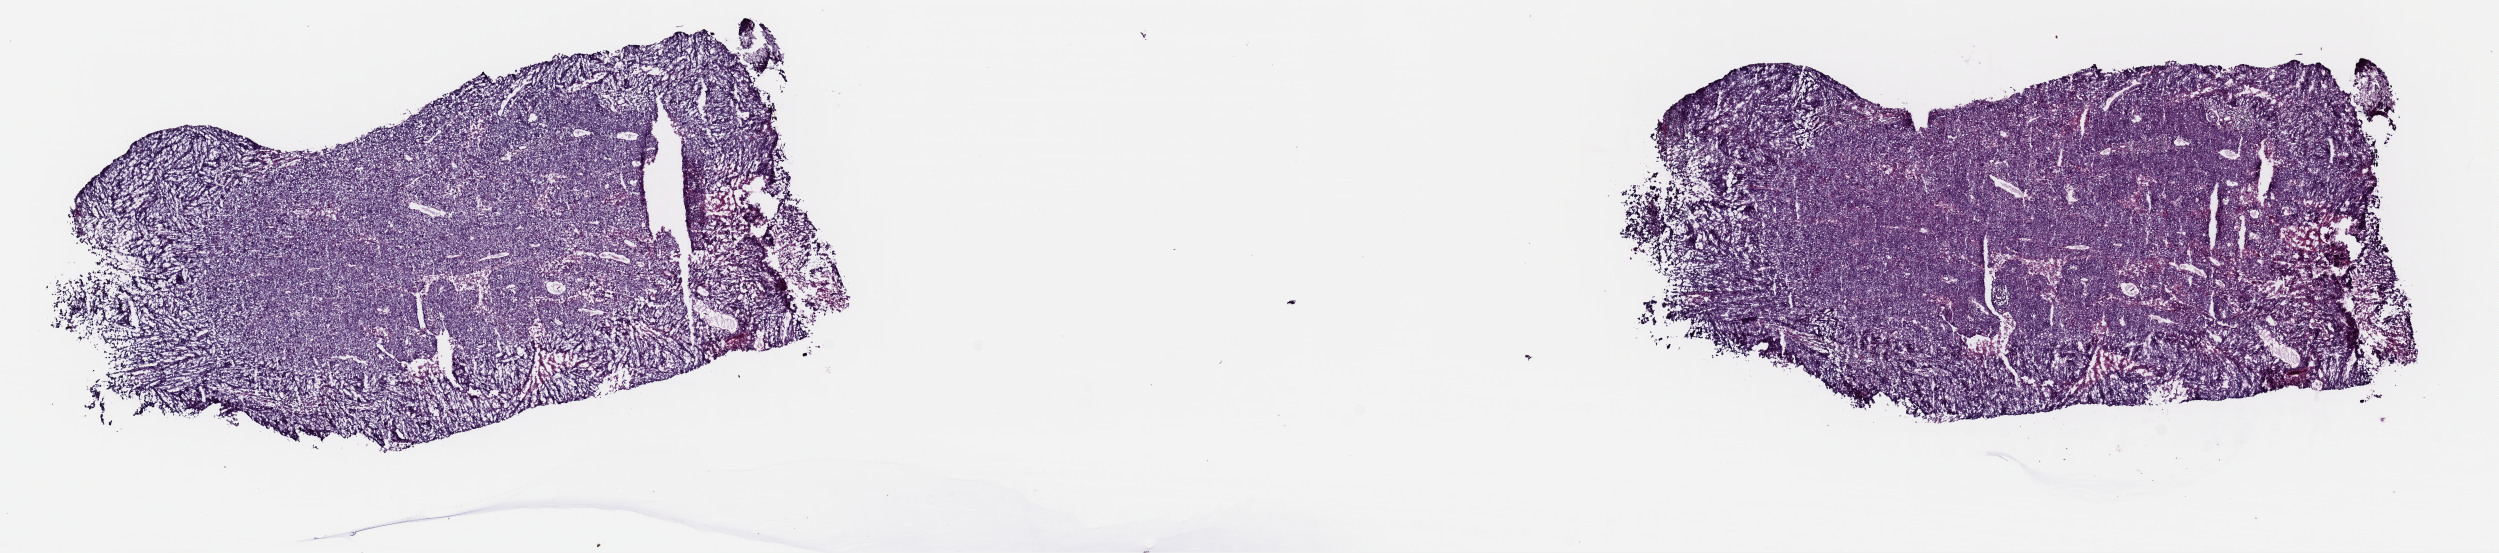
Digitized H&E-stained tissue section (whole slide) — whole scanned area (about 19.7 x 4.4 mm, acquisition: 40x scan) shown as a low-resolution overview; frozen section from the top of the tissue portion; primary tumour sample from the uterus. Patient: female, age at initial diagnosis 70 years. Histologic grade: G3 (poorly differentiated). Composition of this section per pathologist review: tumour cells 70%, tumour nuclei 90%, normal cells 10%, stromal cells 0%, necrosis 20%. Inflammatory infiltration, as recorded: lymphocyte infiltration 20%, monocyte infiltration 0%, neutrophil infiltration 10%.
Lymph nodes positive (case pathology): 0 of 37 examined. Diagnosis: Serous cystadenocarcinoma, NOS (endometrium). FIGO stage: IB.